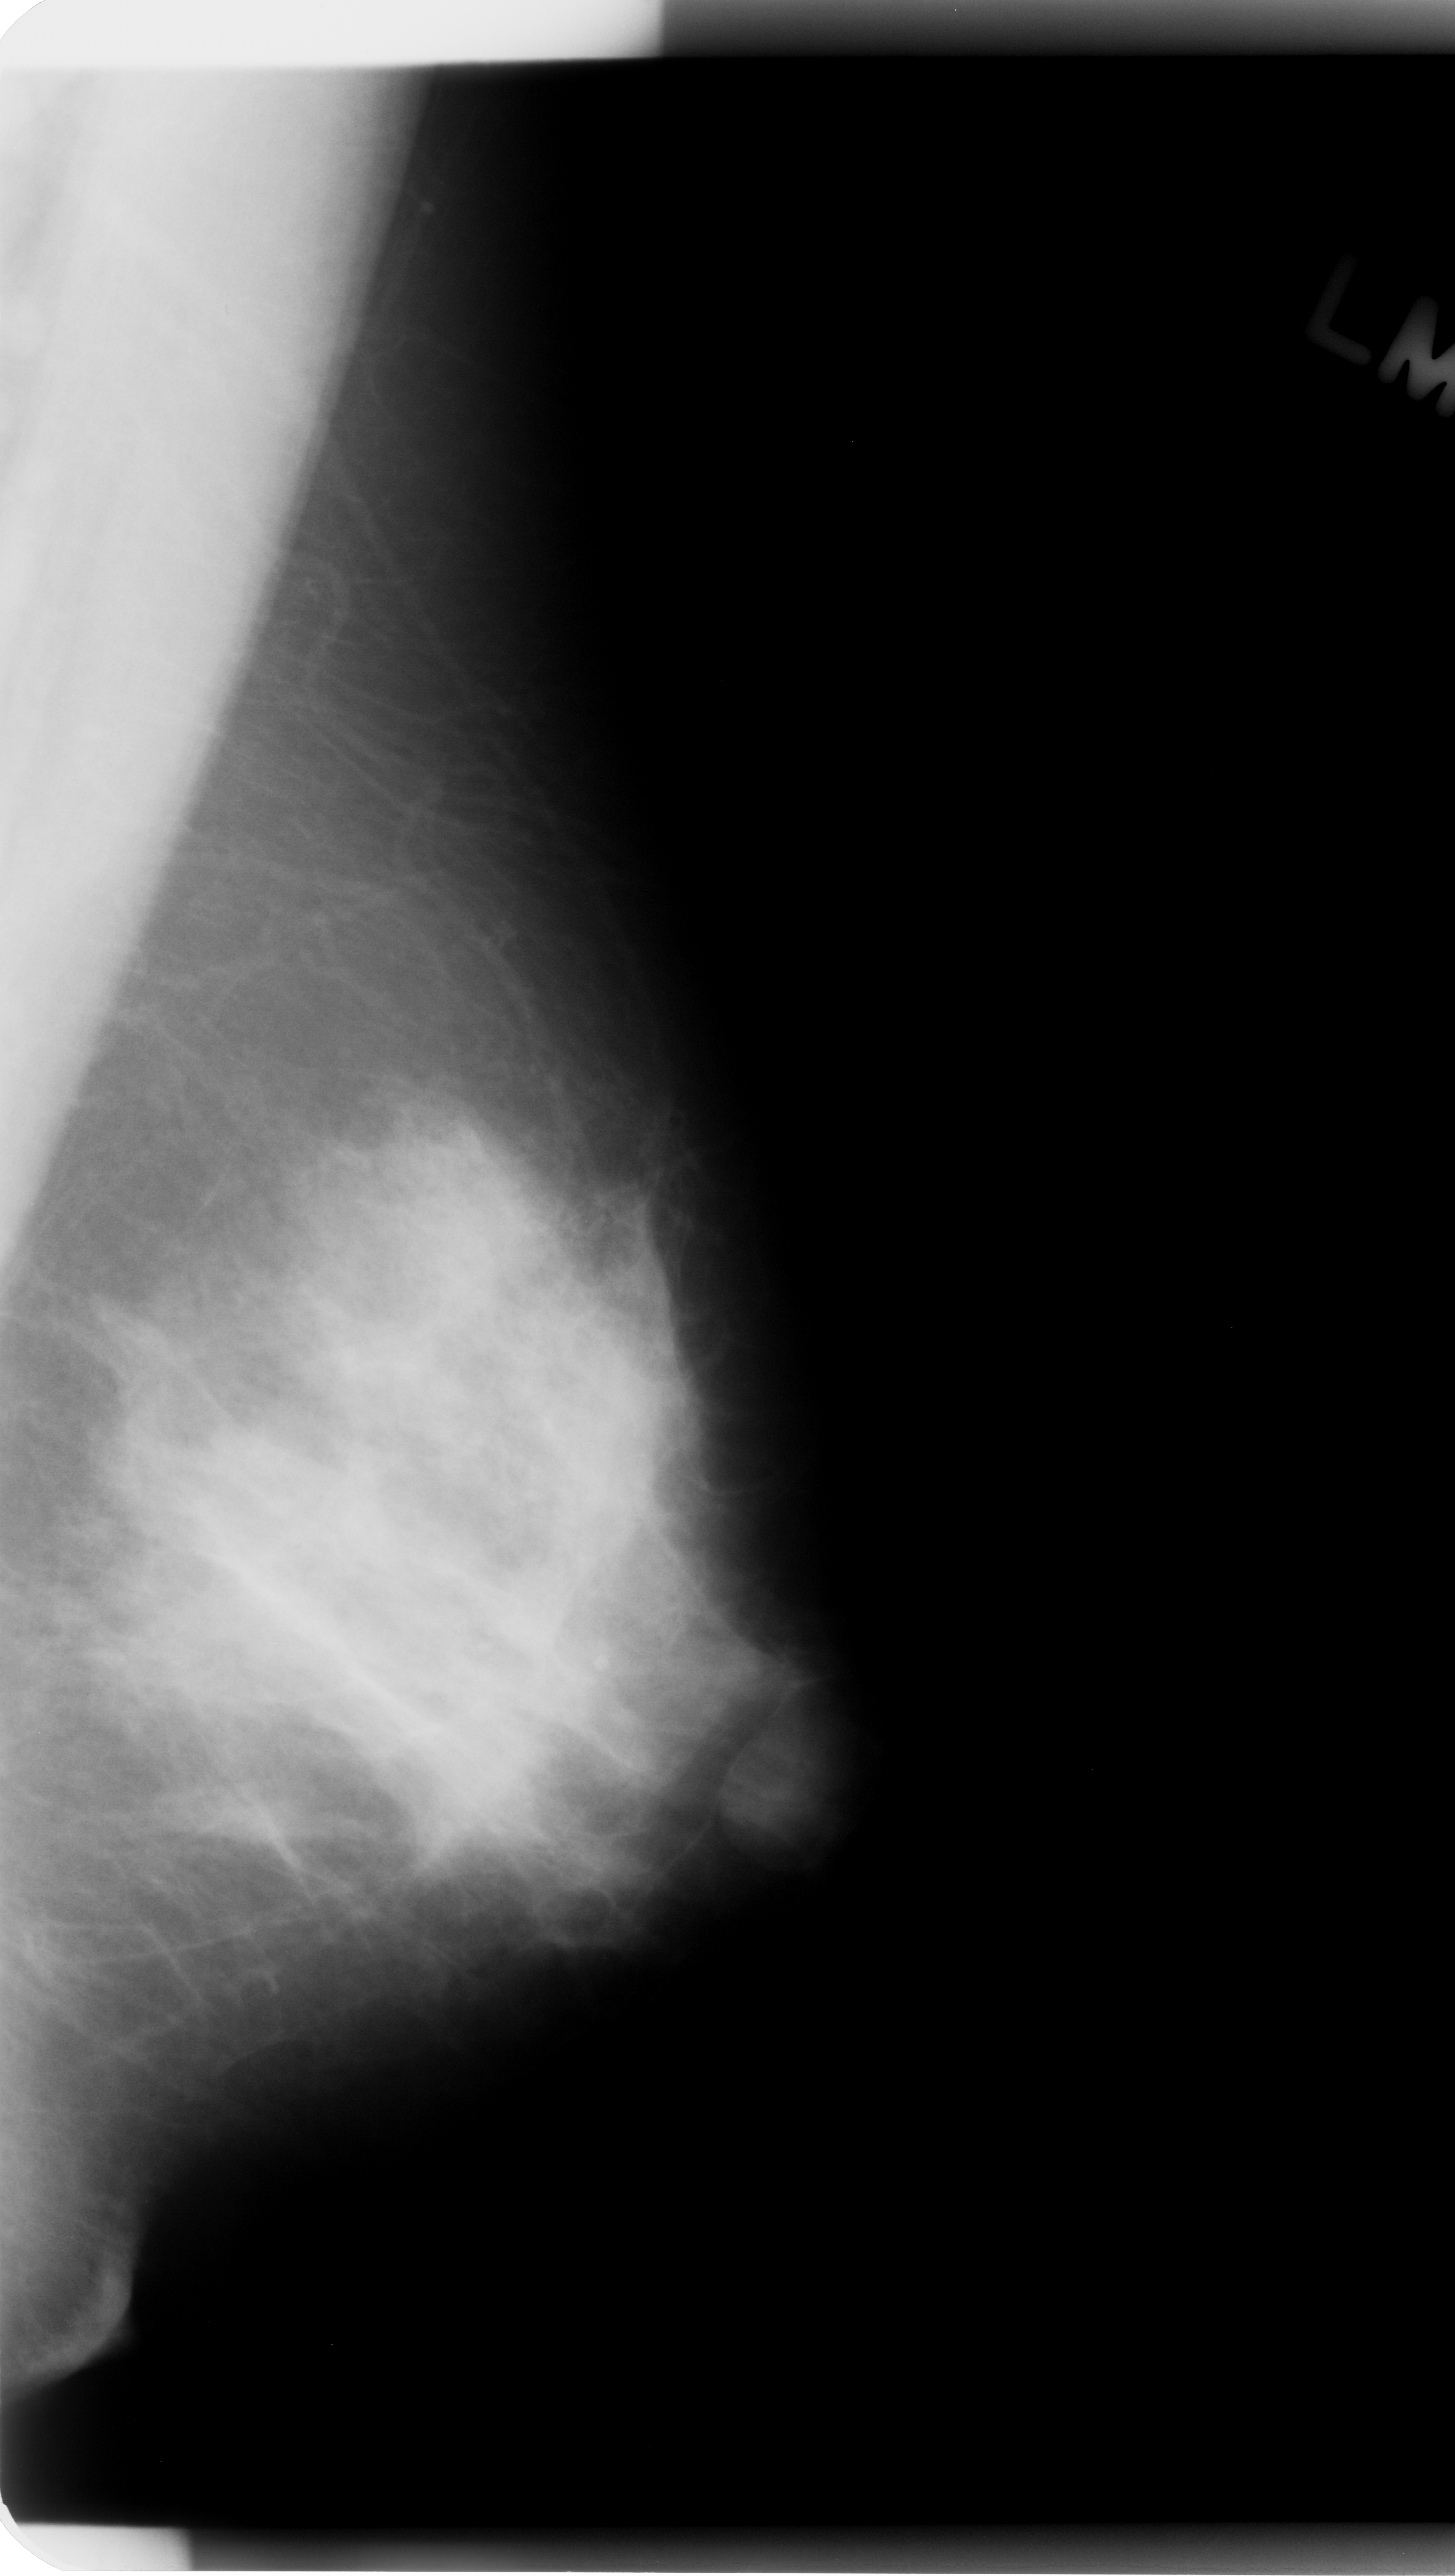
Digitized screen-film mammogram, left breast, mediolateral oblique (MLO) view, breast composition: heterogeneously dense (BI-RADS density category 3 of 4).
- Abnormality record for this image: mass, shape oval, margins circumscribed; BI-RADS assessment category 4; pathology (as recorded): benign.